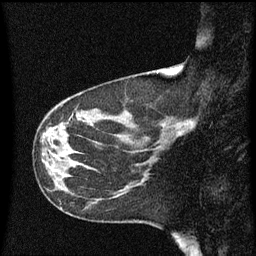
Breast MRI (dynamic contrast-enhanced), one sagittal slice. Slice 23 of 60 in the series (ordered by position). Dynamic contrast-enhanced series, image 2 of 3 at this slice position (ordered by acquisition). 1.5 T. TE 4.2 ms, TR 8.4 ms. 256 × 256 image matrix, field of view 200 × 200 mm. Patient: female, 41 years. From the clinical record (not read from this slice): setting: breast cancer imaged before/during neoadjuvant chemotherapy; receptor status: triple-negative.
Outlined on this slice (semi-automatically segmented with operator editing):
- analysis volume of interest (the breast-tissue region the enhancement analysis was run in; not a lesion): box from (x=158, y=100) to (x=199, y=145) px
- tumour enhancement mask (voxels above the 70 % enhancement threshold inside the analysis volume of interest): (x=190, y=122)–(x=196, y=127)